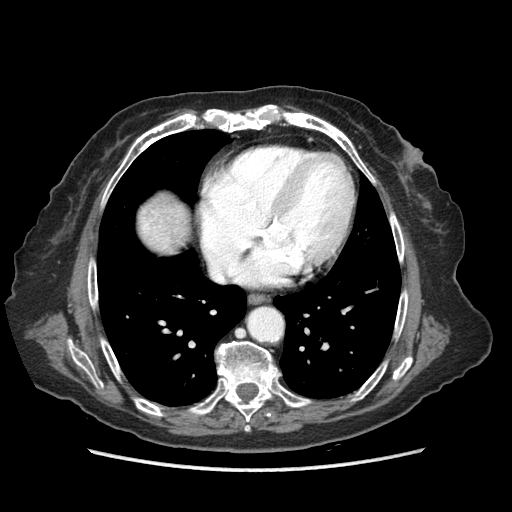
Contrast-enhanced abdominal CT (liver protocol), one axial slice. Position 82 of 89 along the scan axis. Reconstruction kernel STANDARD. 140 kVp. Soft-tissue window (W 400 / L 40 HU). 2.5 mm slice thickness. 512 × 512 image matrix, field of view 360 × 360 mm. Case-level facts recorded for this patient, not image findings: diagnosis: hepatocellular carcinoma (patient treated with transarterial chemoembolisation; whether this scan precedes or follows treatment is not stated here); TNM stage (as recorded): Stage-IIIA; Child-Pugh class: A; tumour differentiation: well differentiated; tumour size: 11 cm.
Annotated regions visible in this slice (semi-automatically segmented with operator editing):
- liver parenchyma outside the tumour (the mass and vessels are separate outlines, so this box may not span the whole liver): bounding box (x1, y1, x2, y2) in pixels: (138, 194, 188, 252)
- liver vessels: (143, 224, 148, 229)